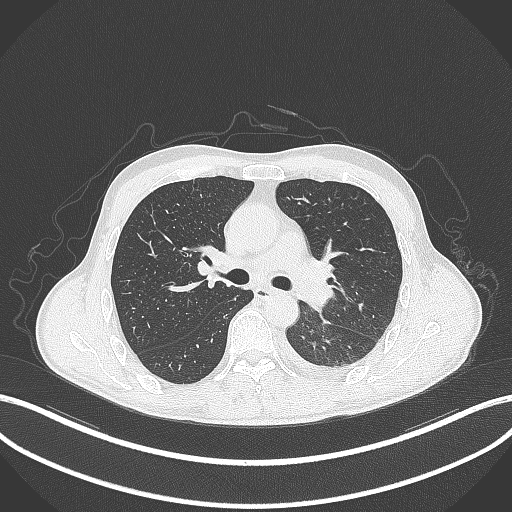
Chest CT, one axial slice. Slice 204 of 295 in the series (ordered by position). 120 kVp. Lung window (W 1500 / L -600 HU). 512 × 512 image matrix, field of view 400 × 400 mm. Male patient, age 47 years. Case-level facts recorded for this patient, not image findings: clinical TNM (as recorded): T3 N1 M1c; histopathological grade: G3.
Annotated regions visible in this slice (rectangle marked by the reading radiologist):
- lung tumour (recorded histology: small cell carcinoma): box from (x=301, y=281) to (x=339, y=313) px